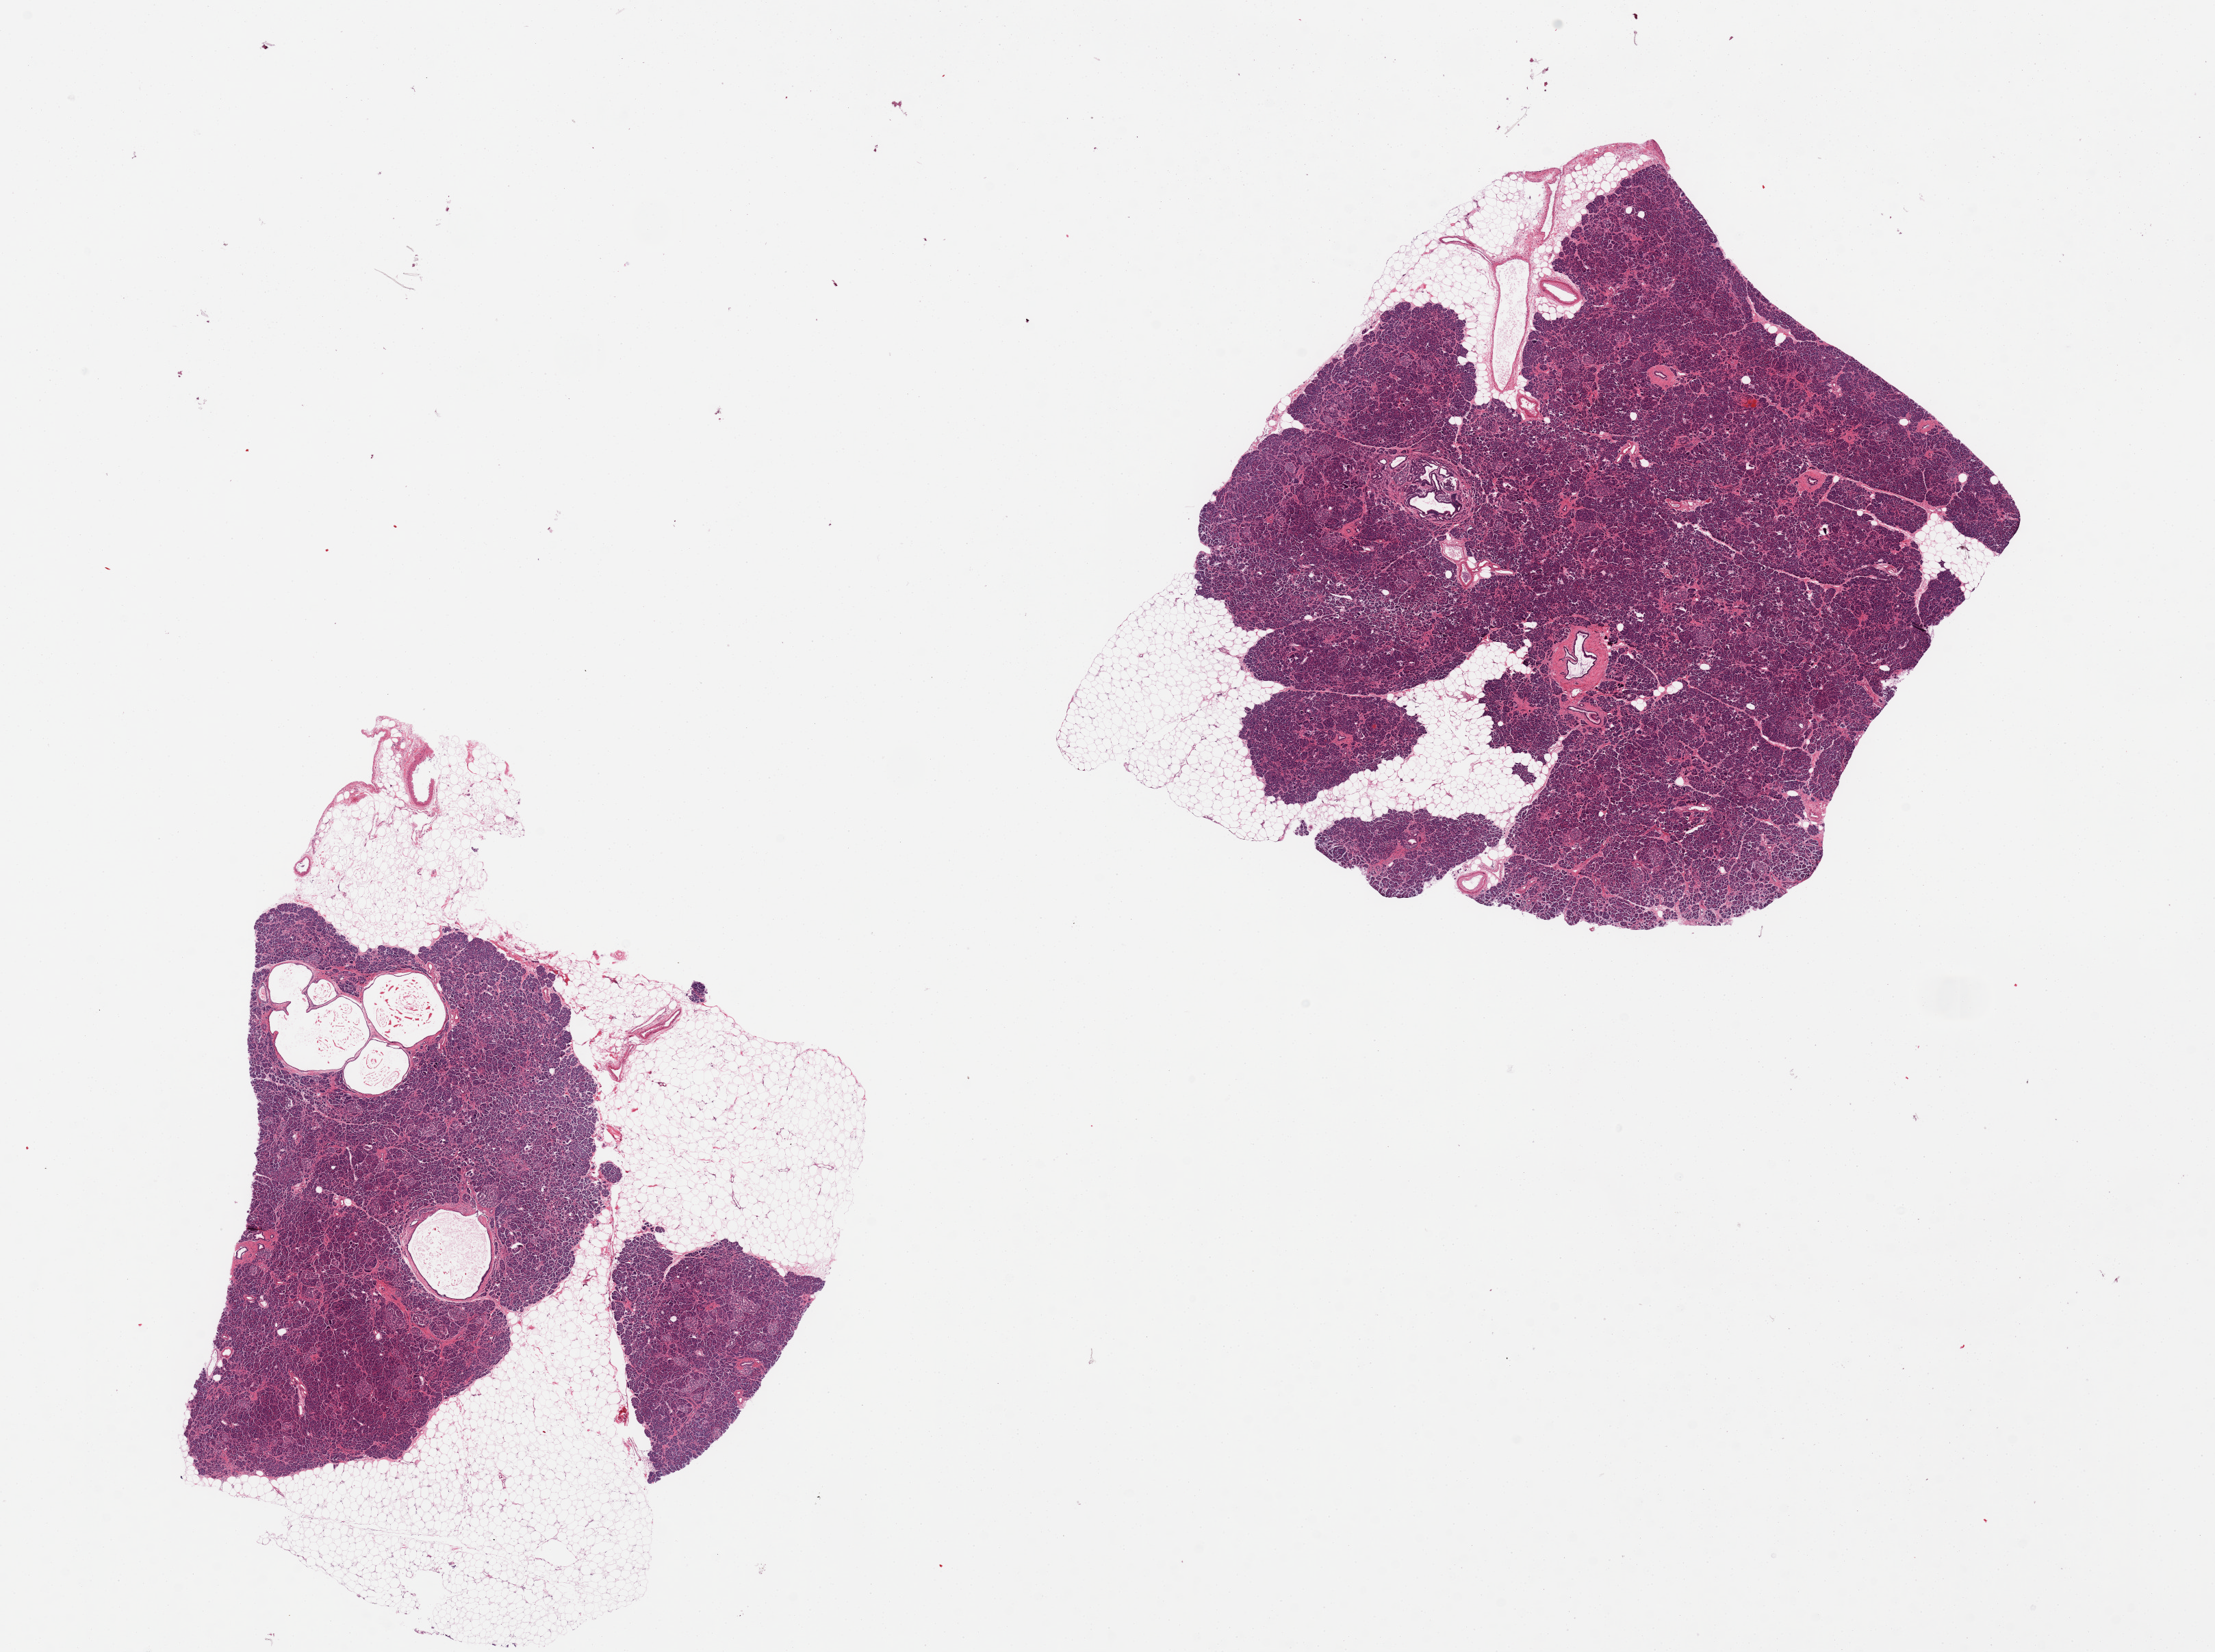
Haematoxylin and eosin whole-slide image, brightfield, whole scanned area (about 25.6 x 19.1 mm) shown as a low-resolution overview; PAXgene-fixed paraffin-embedded (PFPE) section; target tissue: pancreas; tissue donor sample. Donor sex: female.
Pathologist's review note for this sample: 2 pieces, 20-30% fat, focal PanIN-1, dilated ducts vs cyst.